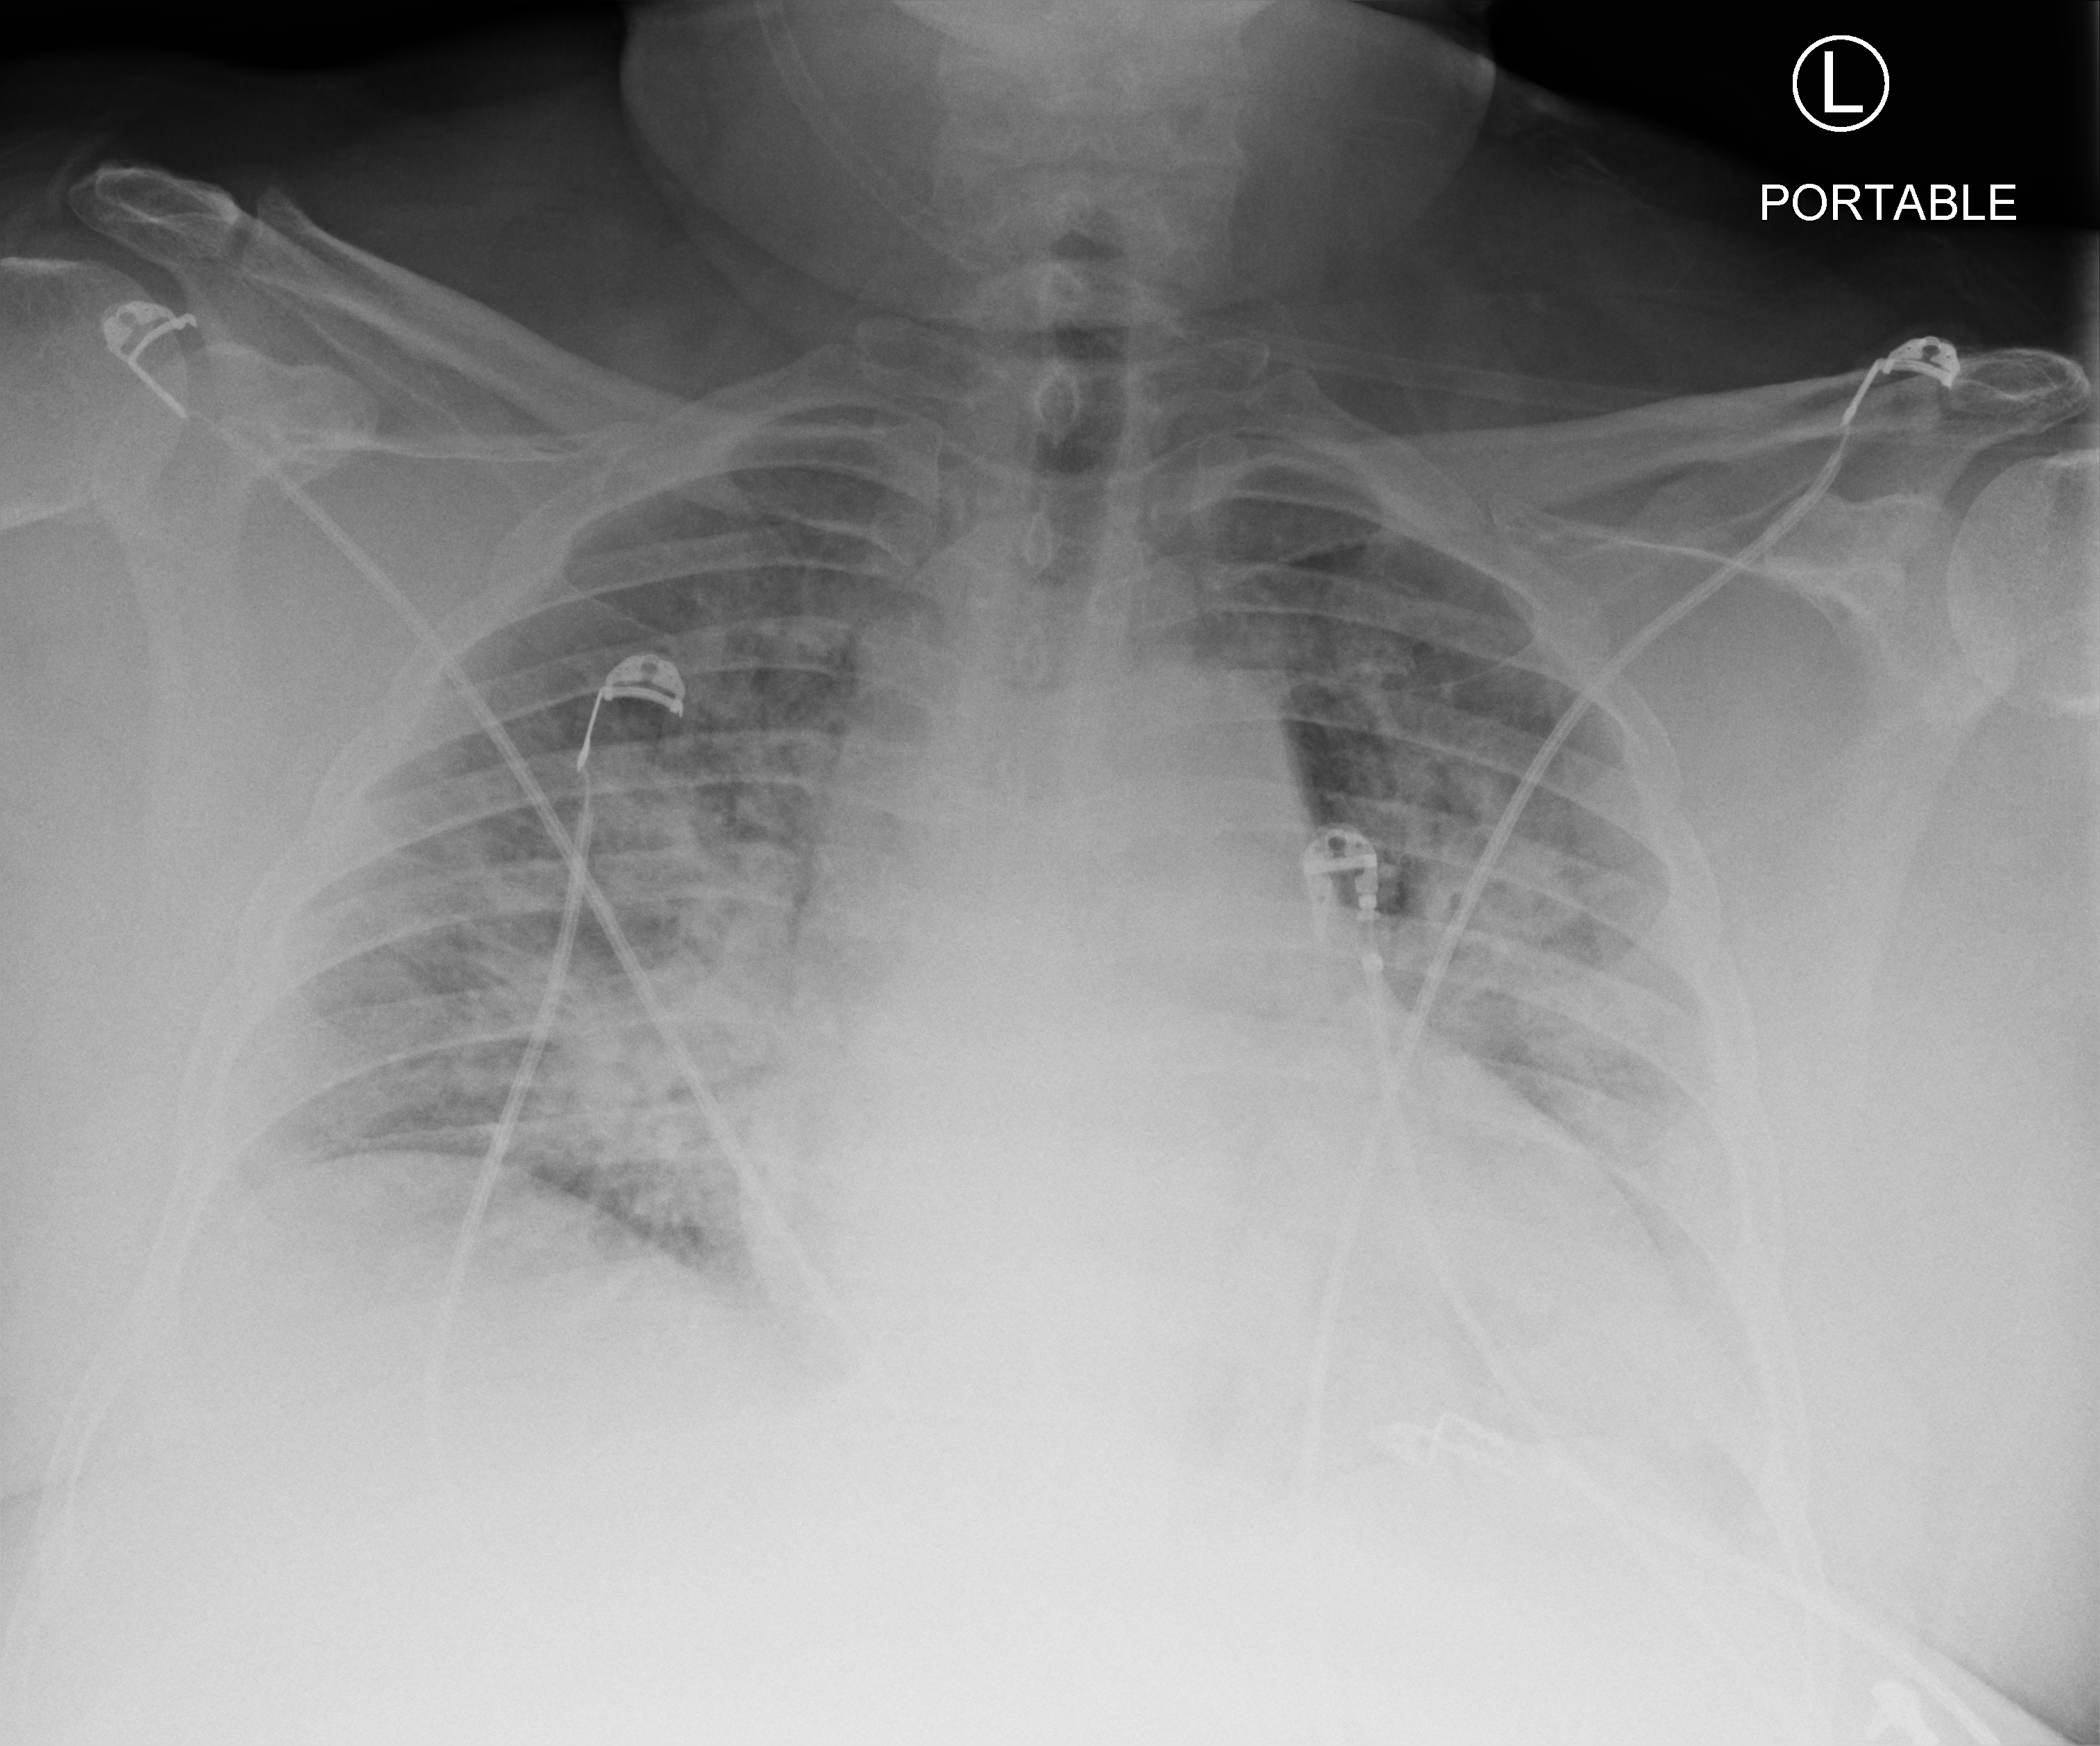
Chest X-ray (portable). Patient hospitalised with COVID-19; male, aged 18–59 years.
From the hospital-stay record, not from the radiograph (when in the stay this image was taken is not recorded):
- hypertension (admission record): no